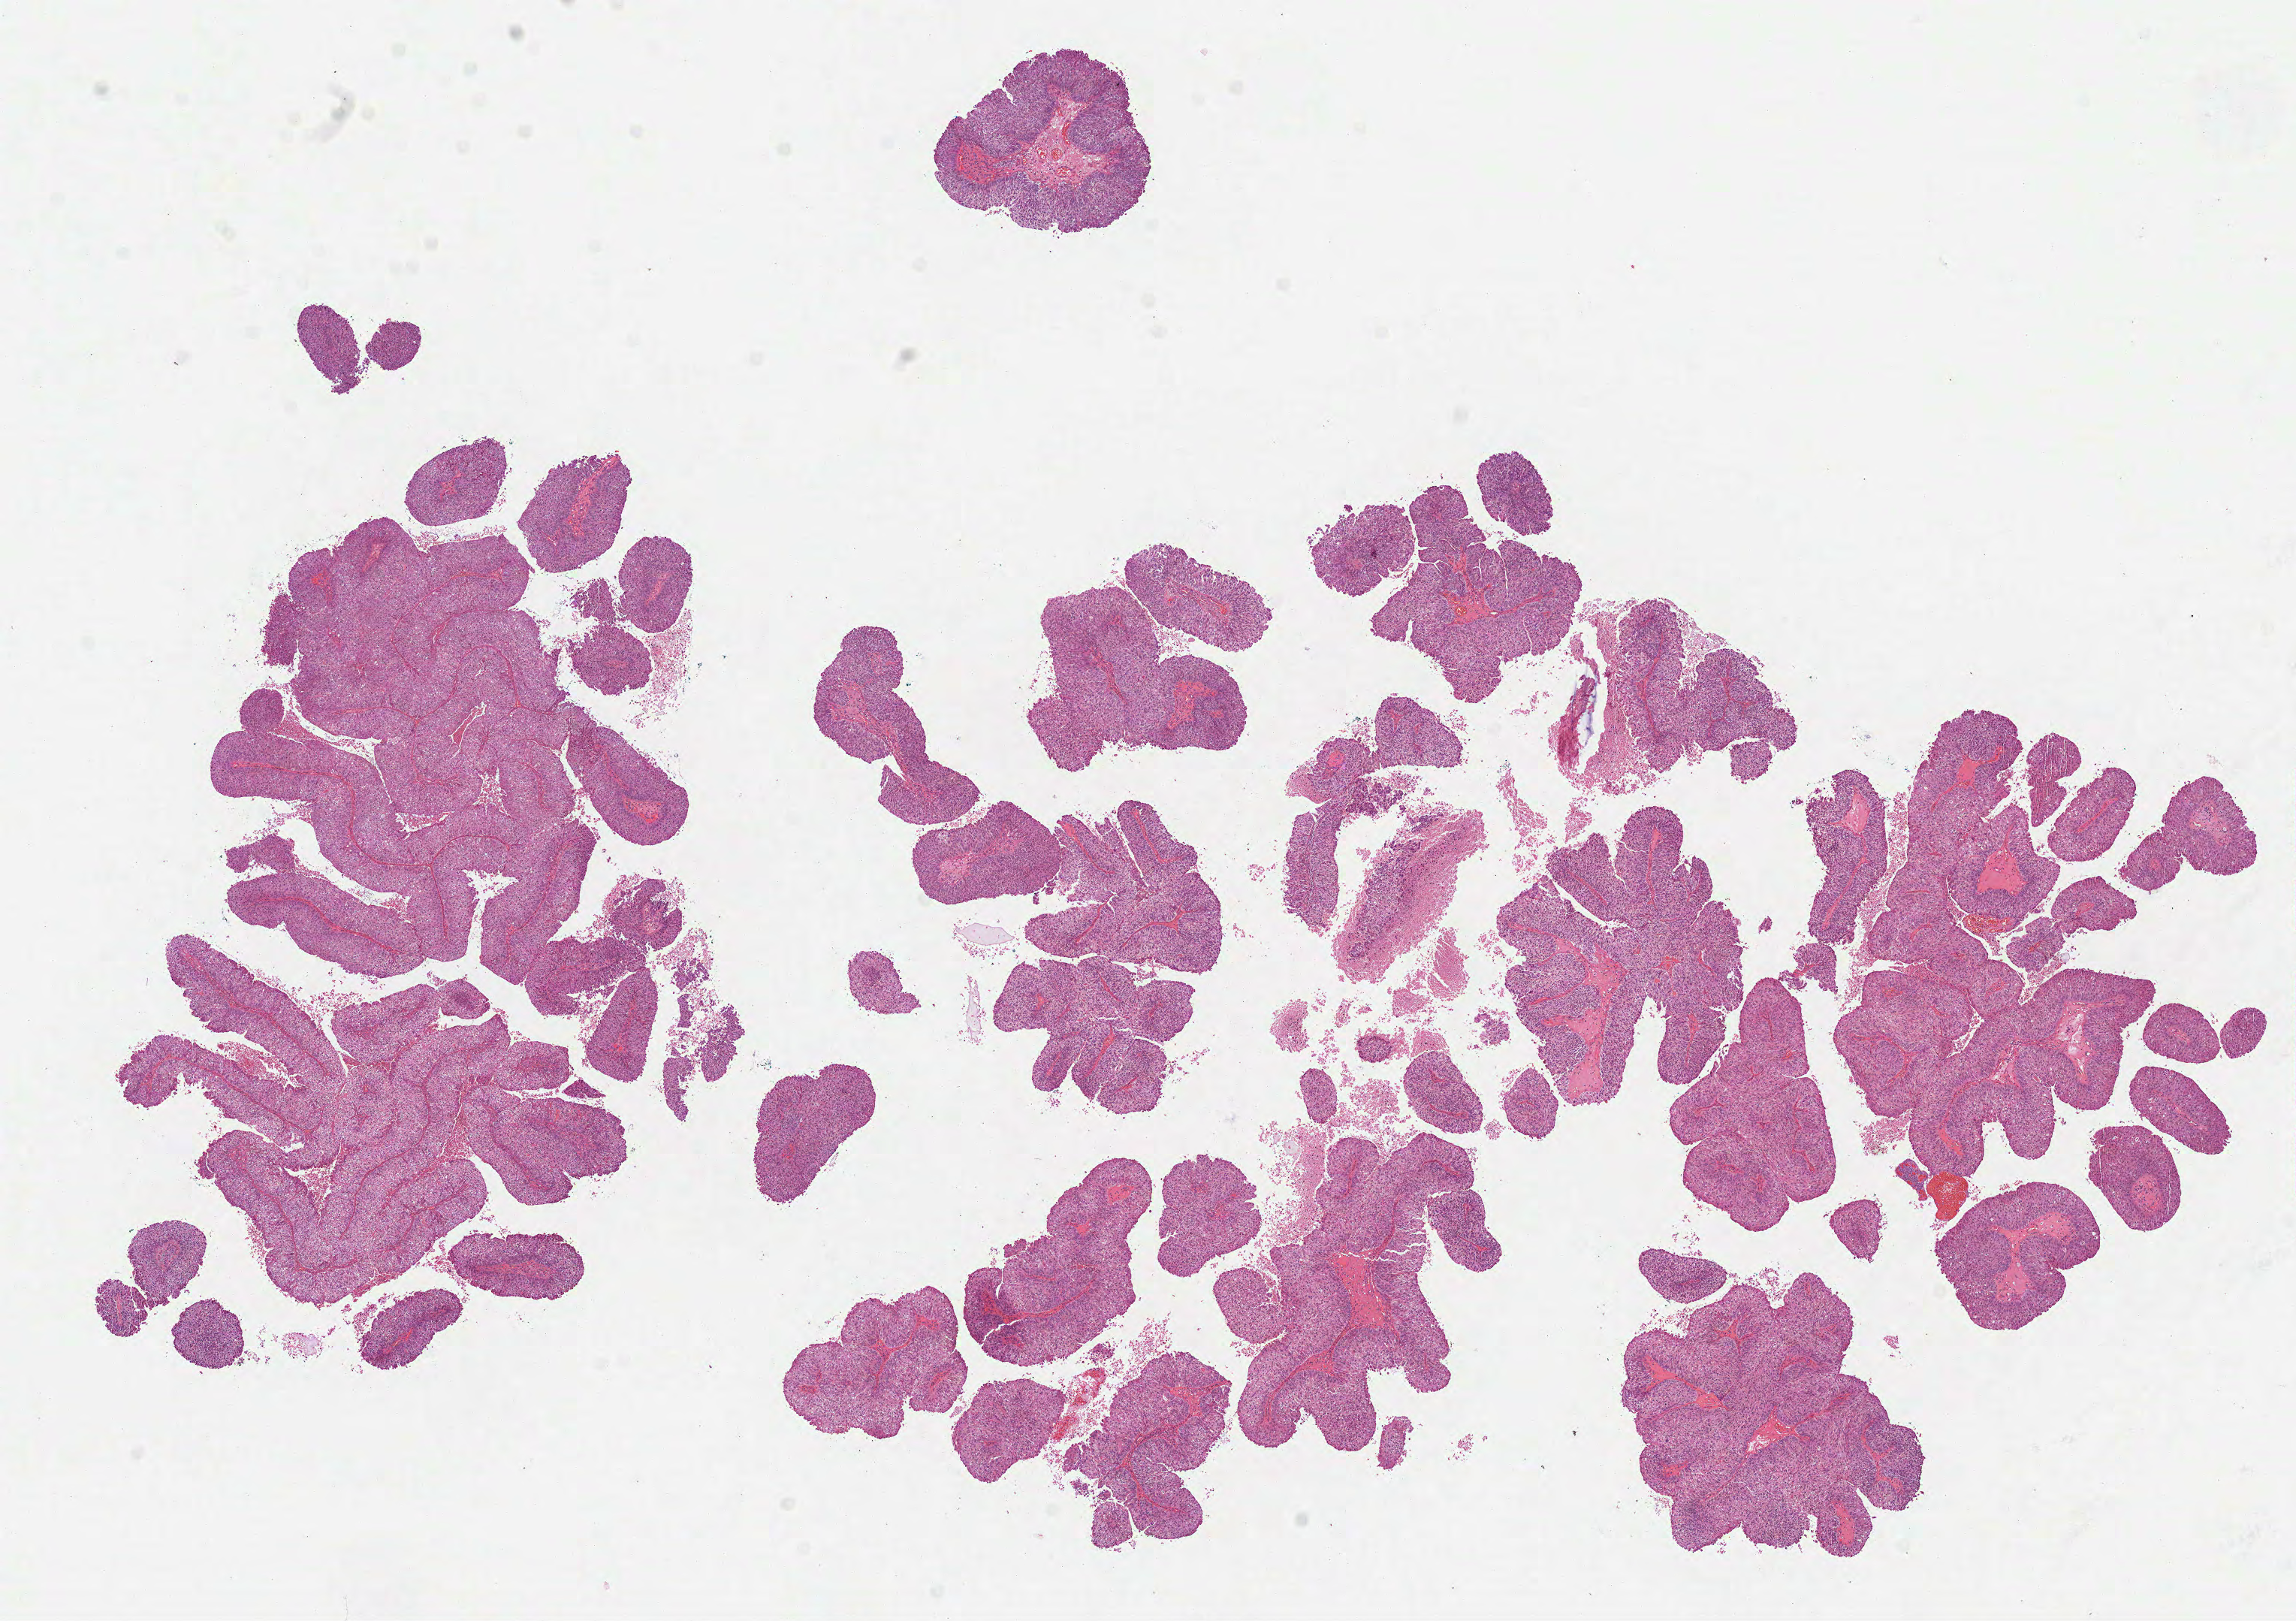
Hematoxylin and eosin (H&E) stained whole-slide image, shown as a low-resolution overview of the whole scanned area (about 12.3 x 8.7 mm); FFPE section; primary tumour sample from the kidney. Patient: female, age at initial diagnosis 75 years.
* AJCC pathologic stage: I (7th edition)
* histologic diagnosis: Papillary adenocarcinoma, NOS